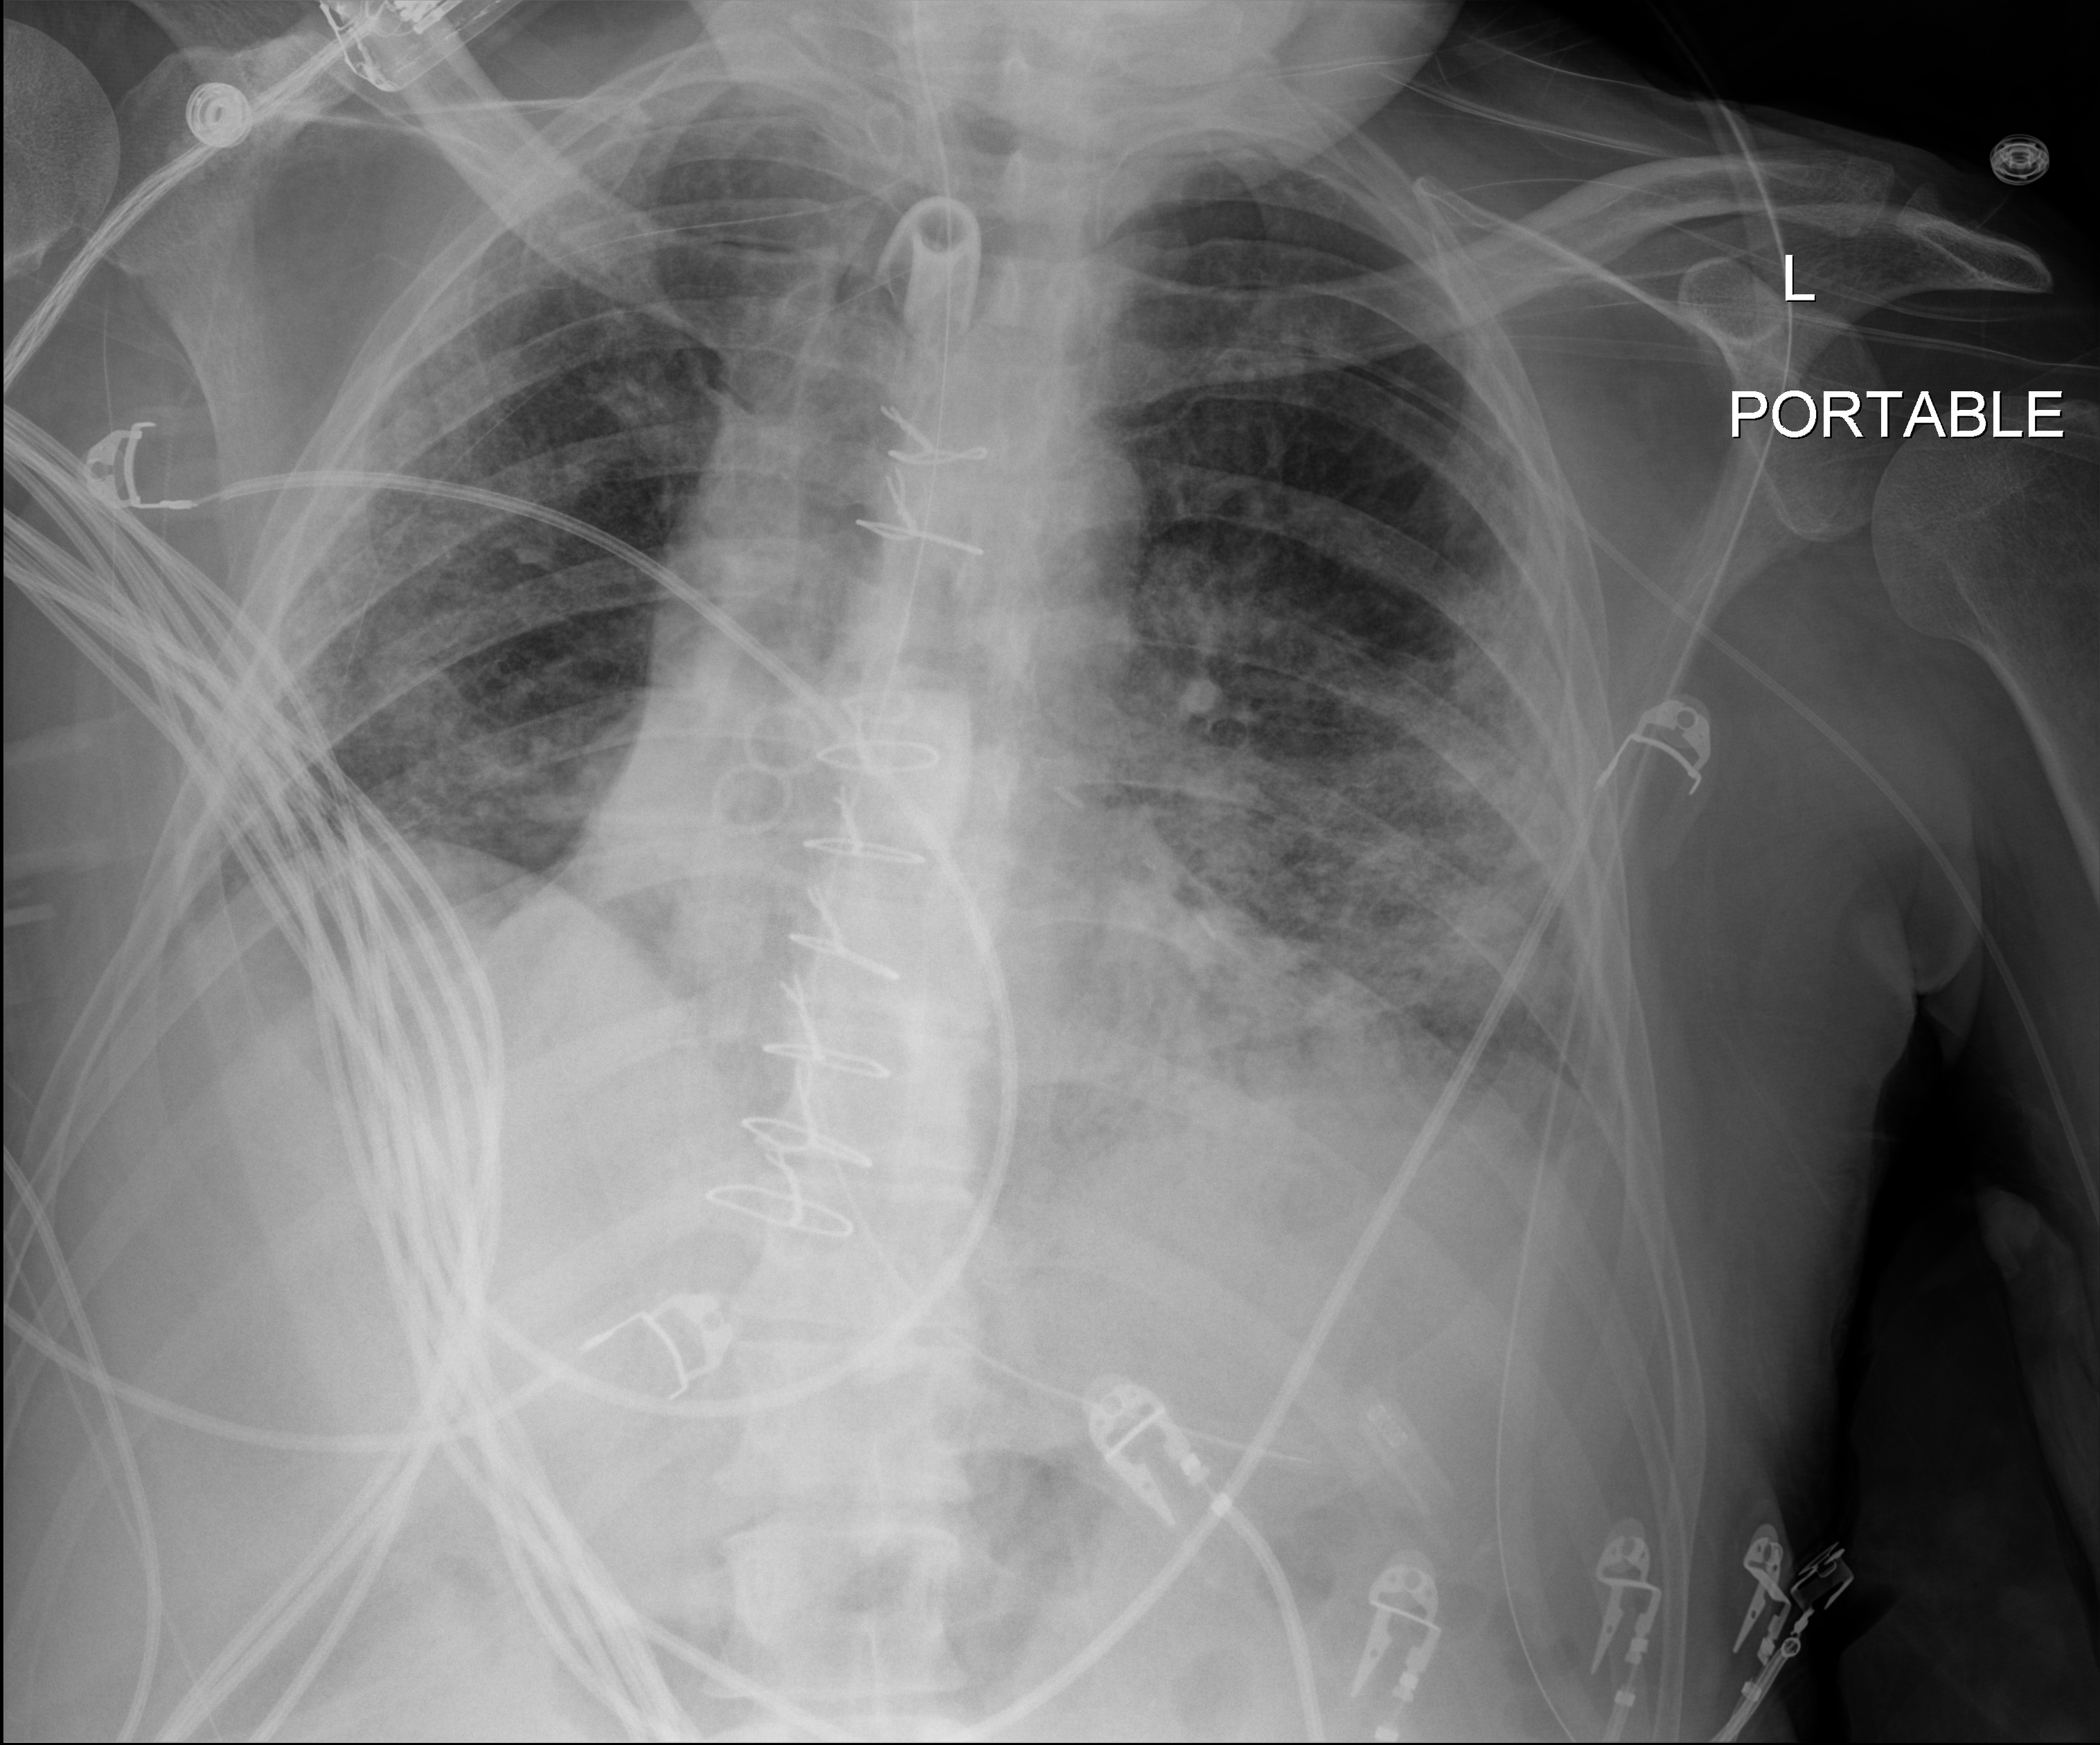
Chest X-ray. Patient hospitalised with COVID-19; male, aged 18–59 years.
From the hospital-stay record, not from the radiograph (when in the stay this image was taken is not recorded):
- mechanically ventilated during this hospital stay: yes
- length of hospital stay: 63 days